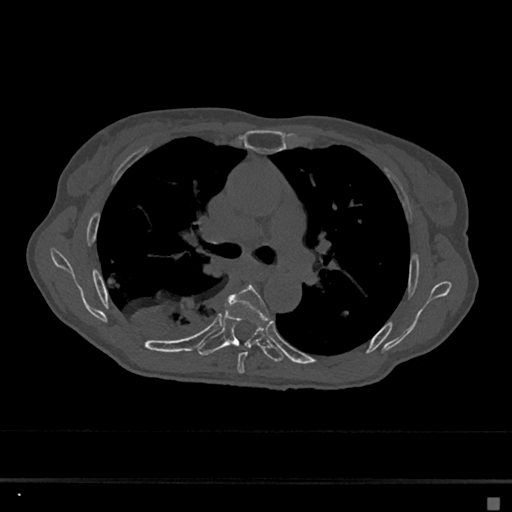
CT including the spine, one axial slice; position 438 of 797 along the scan axis; reconstruction kernel Br40s/3; 120 kVp; bone window (W 1800 / L 400 HU); 0.5 mm slice thickness; 512 × 512 image matrix. Patient: female, 68 years. From the clinical record (not read from this slice): primary cancer: renal.
Annotated regions visible in this slice (semi-automatically segmented with operator editing):
- T5 vertebra: bounding box <226,285,270,374> (left, top, right, bottom; pixels)
- T6 vertebra: <197,308,283,362>